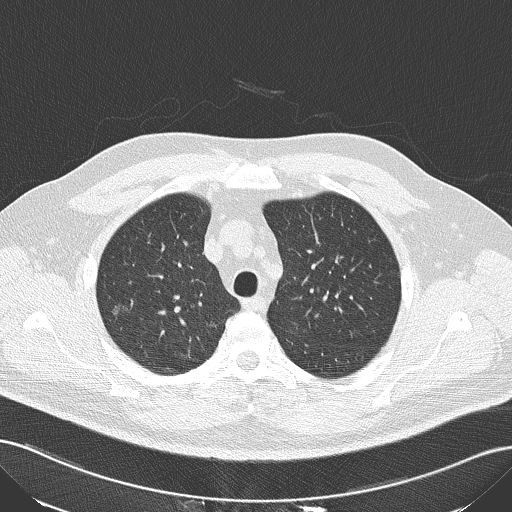
Low-dose screening chest CT, axial slice. Second annual screen. Lung window (W 1500 / L -600 HU). 2 mm slice thickness. Lung (sharp) reconstruction kernel (B50f). 120 kVp. Male, age 56 years at enrolment. Current smoker at enrolment.
- Expert-annotated lung lesion, bounding box [x1, y1, x2, y2] px = [95, 288, 144, 332].
- Reader record for this screening exam (exam-level; its link to the box is not recorded): non-calcified nodule or mass ≥4 mm, right upper lobe, 10 × 9 mm, spiculated (stellate) margins, soft tissue attenuation, pre-existing on the prior screen: no.
- Official screen result: positive, other.
- Participant outcome: lung cancer diagnosed 117 days after this screen — squamous cell carcinoma, NOS, right upper lobe, moderately differentiated (G2), stage IA (AJCC 6th edition), 10 mm at pathology.